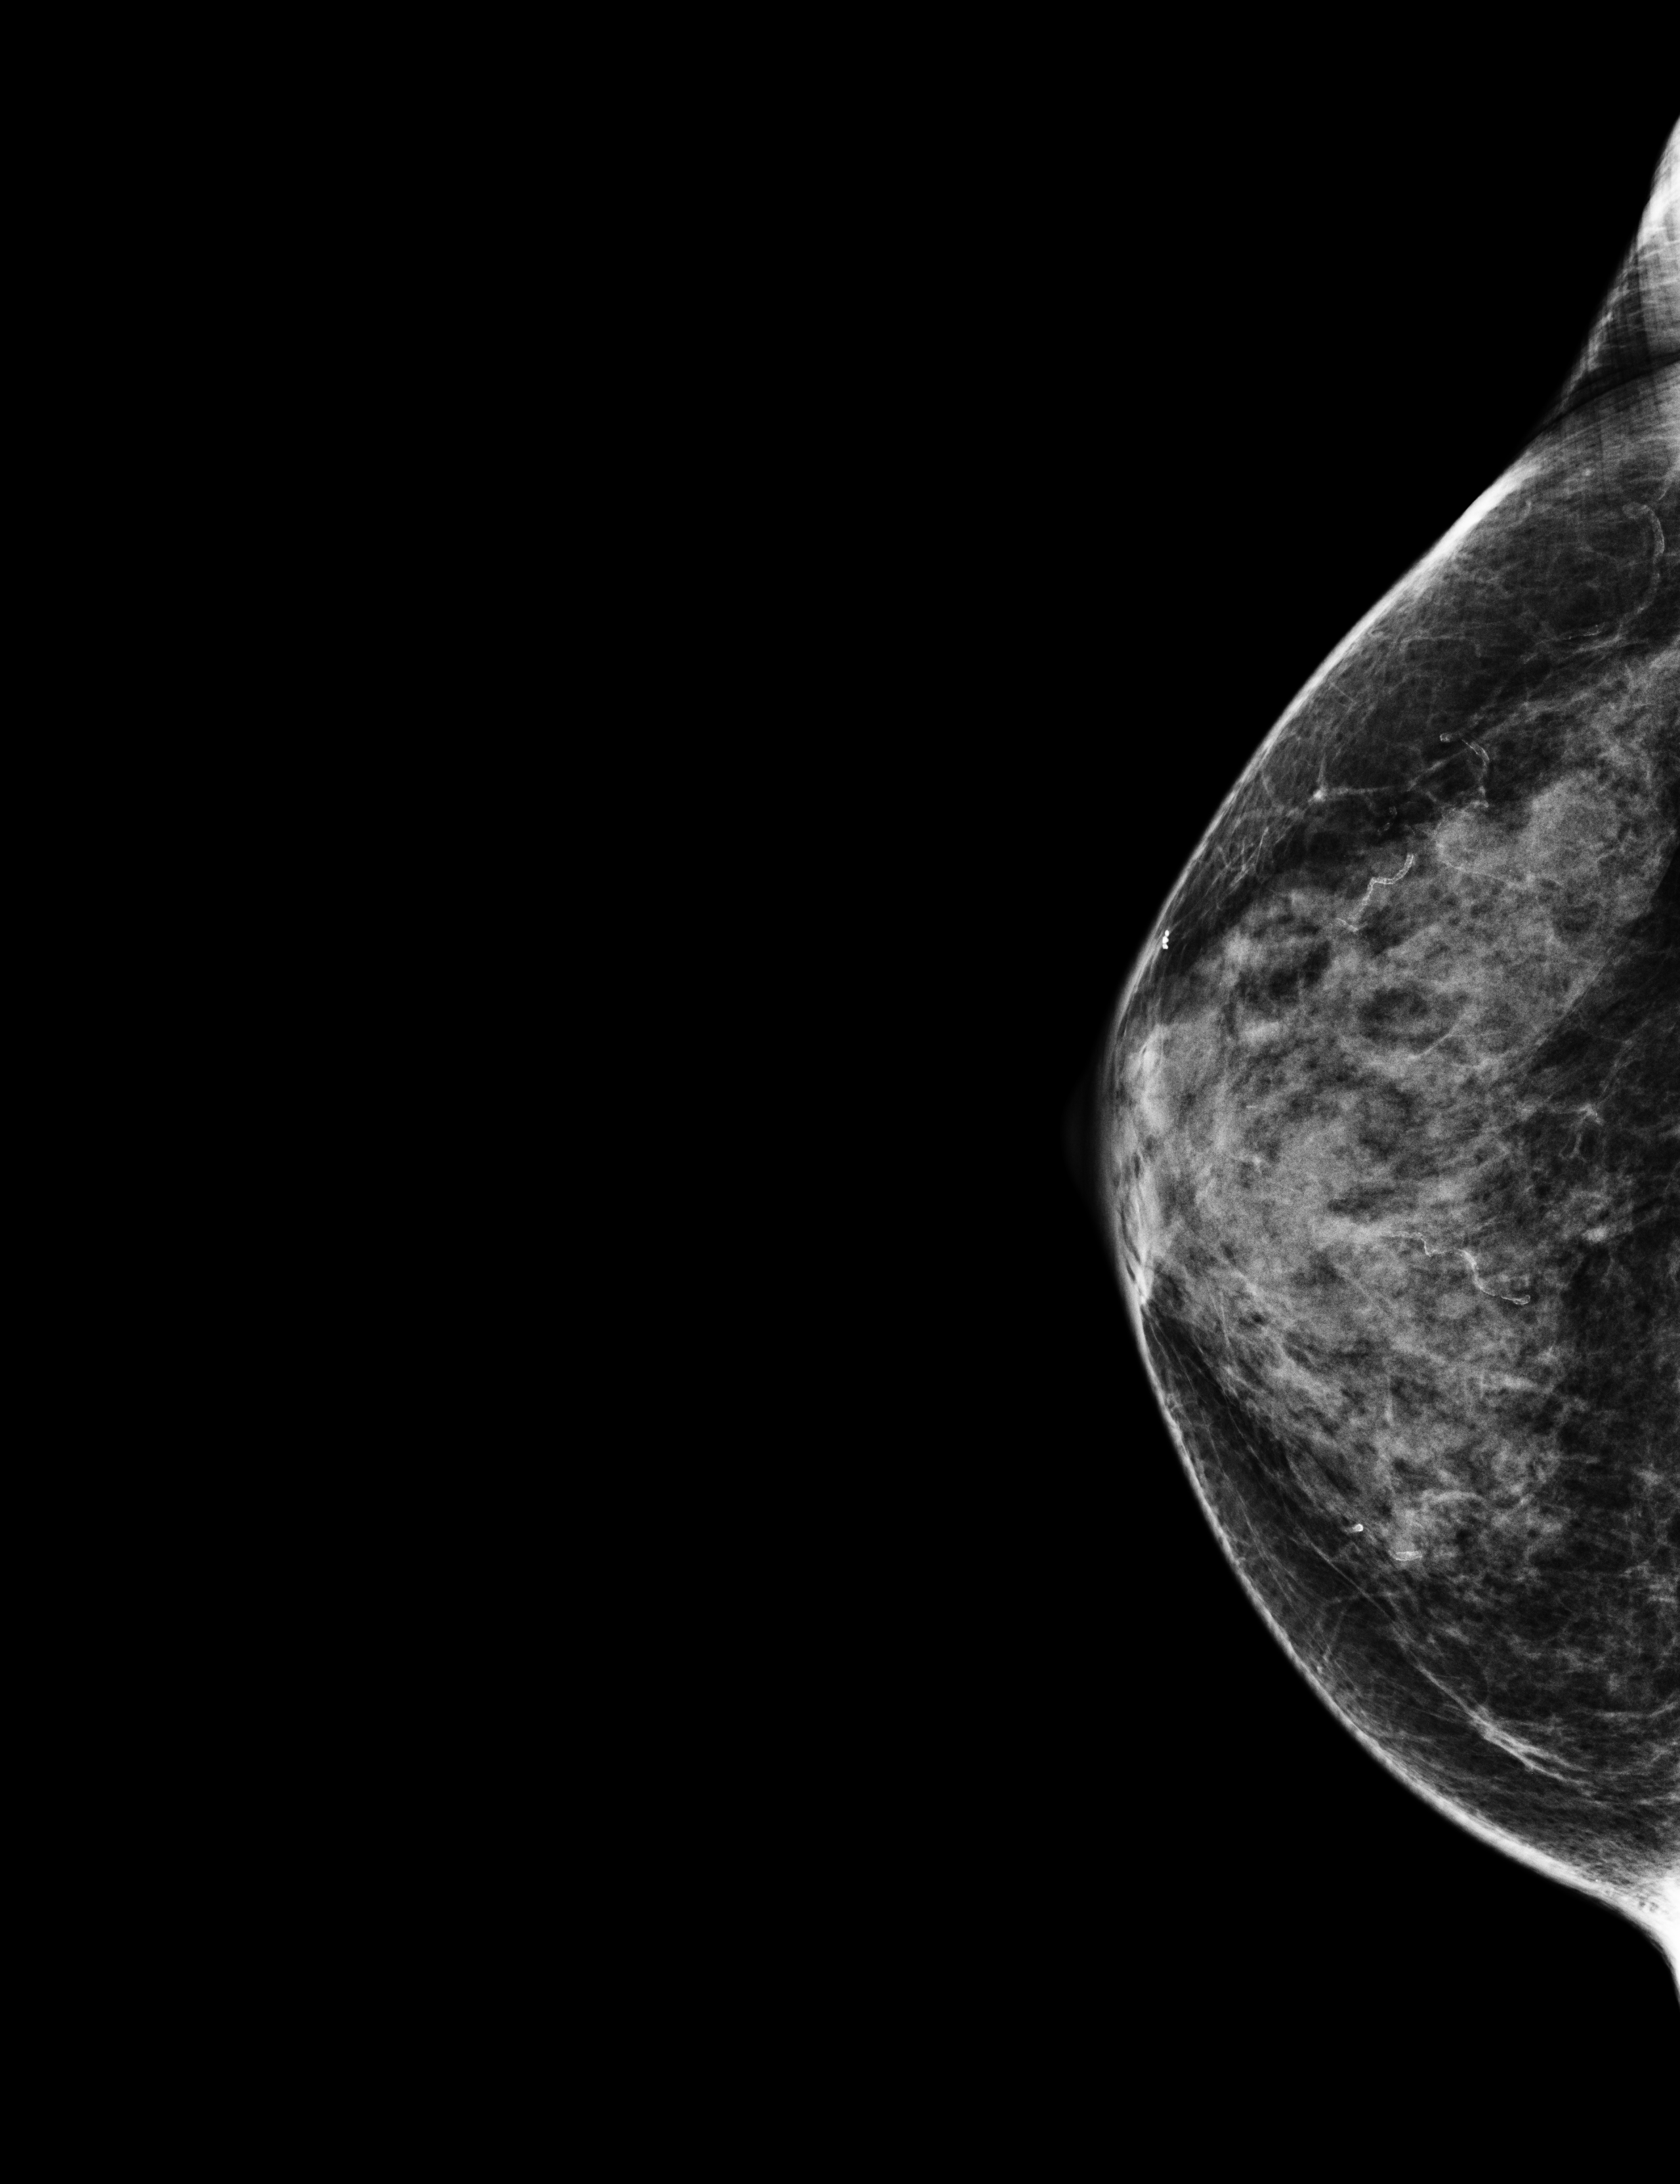
Annual screening mammography examination, compressed breast thickness 39 mm. Patient aged 65 years (female).
Image type: full-field digital mammogram. Breast: right. Projection: CC view.